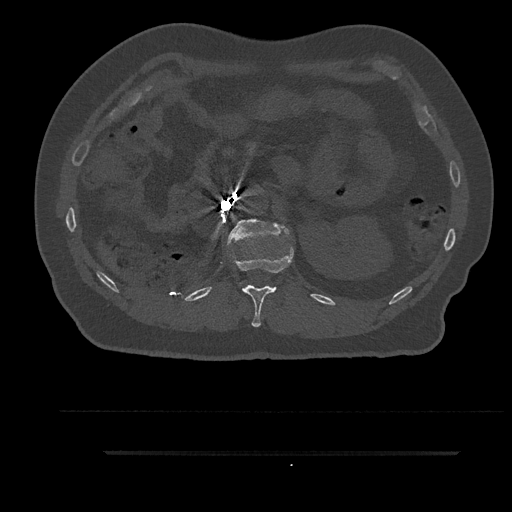
CT including the spine, one axial slice; slice 219 of 797 in the series (ordered by position); reconstruction kernel Br40s/3; 120 kVp; bone window (W 1800 / L 400 HU); 0.5 mm slice thickness; 512 × 512 image matrix. Patient: male, 63 years. Case-level facts recorded for this patient, not image findings: primary cancer: renal.
Annotated regions visible in this slice (semi-automatically segmented with operator editing):
- L1 vertebra: bounding box [x1, y1, x2, y2] px = [227, 219, 289, 245]
- T12 vertebra: [231, 247, 294, 328]